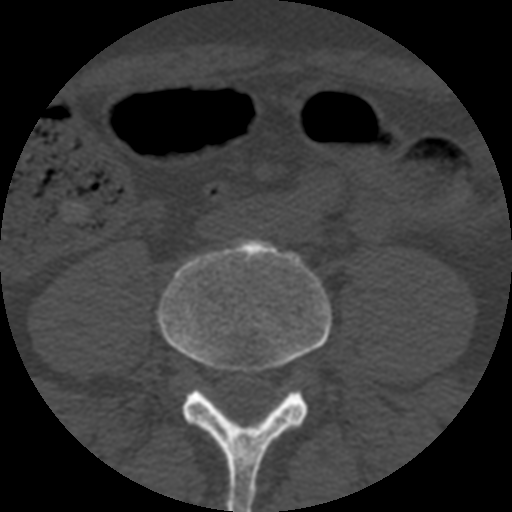
CT including the spine, one axial slice; slice 85 of 508 in the series (ordered by position); reconstruction kernel STANDARD; 120 kVp; bone window (W 1800 / L 400 HU); 1.25 mm slice thickness; 512 × 512 image matrix, field of view 160 × 160 mm. Patient age 57 years. Case-level facts recorded for this patient, not image findings: primary cancer: prostate.
Outlined on this slice (semi-automatically segmented with operator editing):
- L4 vertebra: bounding box (x1, y1, x2, y2) in pixels: (158, 240, 331, 512)